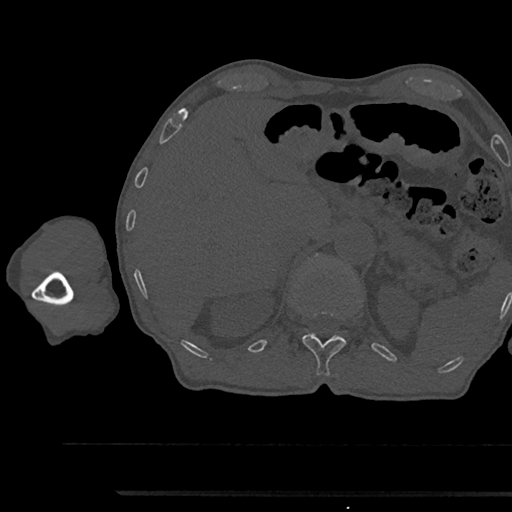
CT including the spine, one axial slice; slice 691 of 797 in the series (ordered by position); reconstruction kernel Br40s/3; 120 kVp; bone window (W 1800 / L 400 HU); 0.5 mm slice thickness; 512 × 512 image matrix. Patient: male, 79 years. Case-level facts recorded for this patient, not image findings: primary cancer: prostate.
Outlined on this slice (semi-automatic segmentation, software-assisted and operator-edited):
- L1 vertebra: bounding box [x1, y1, x2, y2] px = [315, 255, 321, 259]
- T12 vertebra: [302, 333, 347, 376]